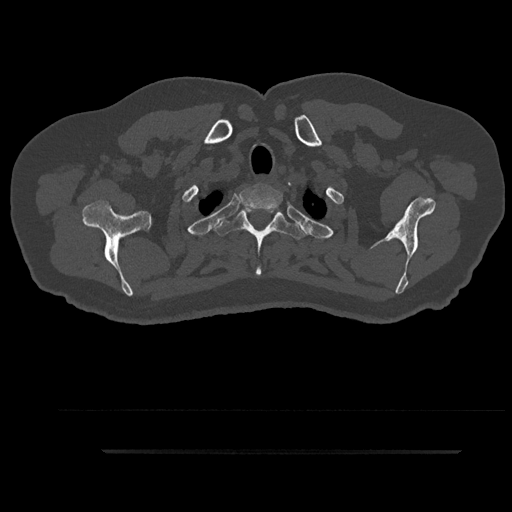
CT including the spine, one axial slice; position 771 of 797 along the scan axis; bone window (W 1800 / L 400 HU); 512 × 512 image matrix, field of view 432 × 432 mm. Male patient, age 63 years. From the clinical record (not read from this slice): primary cancer: renal.
Annotated regions visible in this slice (semi-automatically segmented with operator editing):
- T1 vertebra: bounding box <239,185,283,219> (left, top, right, bottom; pixels)
- T2 vertebra: <213,206,306,276>